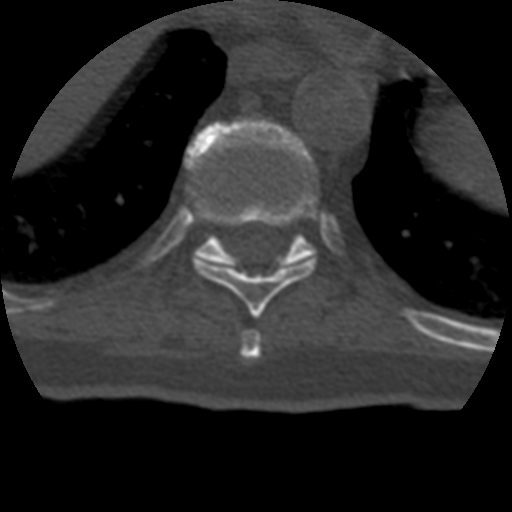
CT including the spine, one axial slice. Slice 232 of 399 in the series (ordered by position). Reconstruction kernel STANDARD. Bone window (W 1800 / L 400 HU). 1.25 mm slice thickness. 512 × 512 image matrix, field of view 160 × 160 mm. Patient age 69 years. From the clinical record (not read from this slice): primary cancer: prostate.
Outlined on this slice (semi-automatic segmentation, software-assisted and operator-edited):
- T10 vertebra: box from (x=185, y=119) to (x=316, y=266) px
- T8 vertebra: (x=241, y=330)–(x=262, y=359)
- T9 vertebra: (x=196, y=178)–(x=316, y=317)